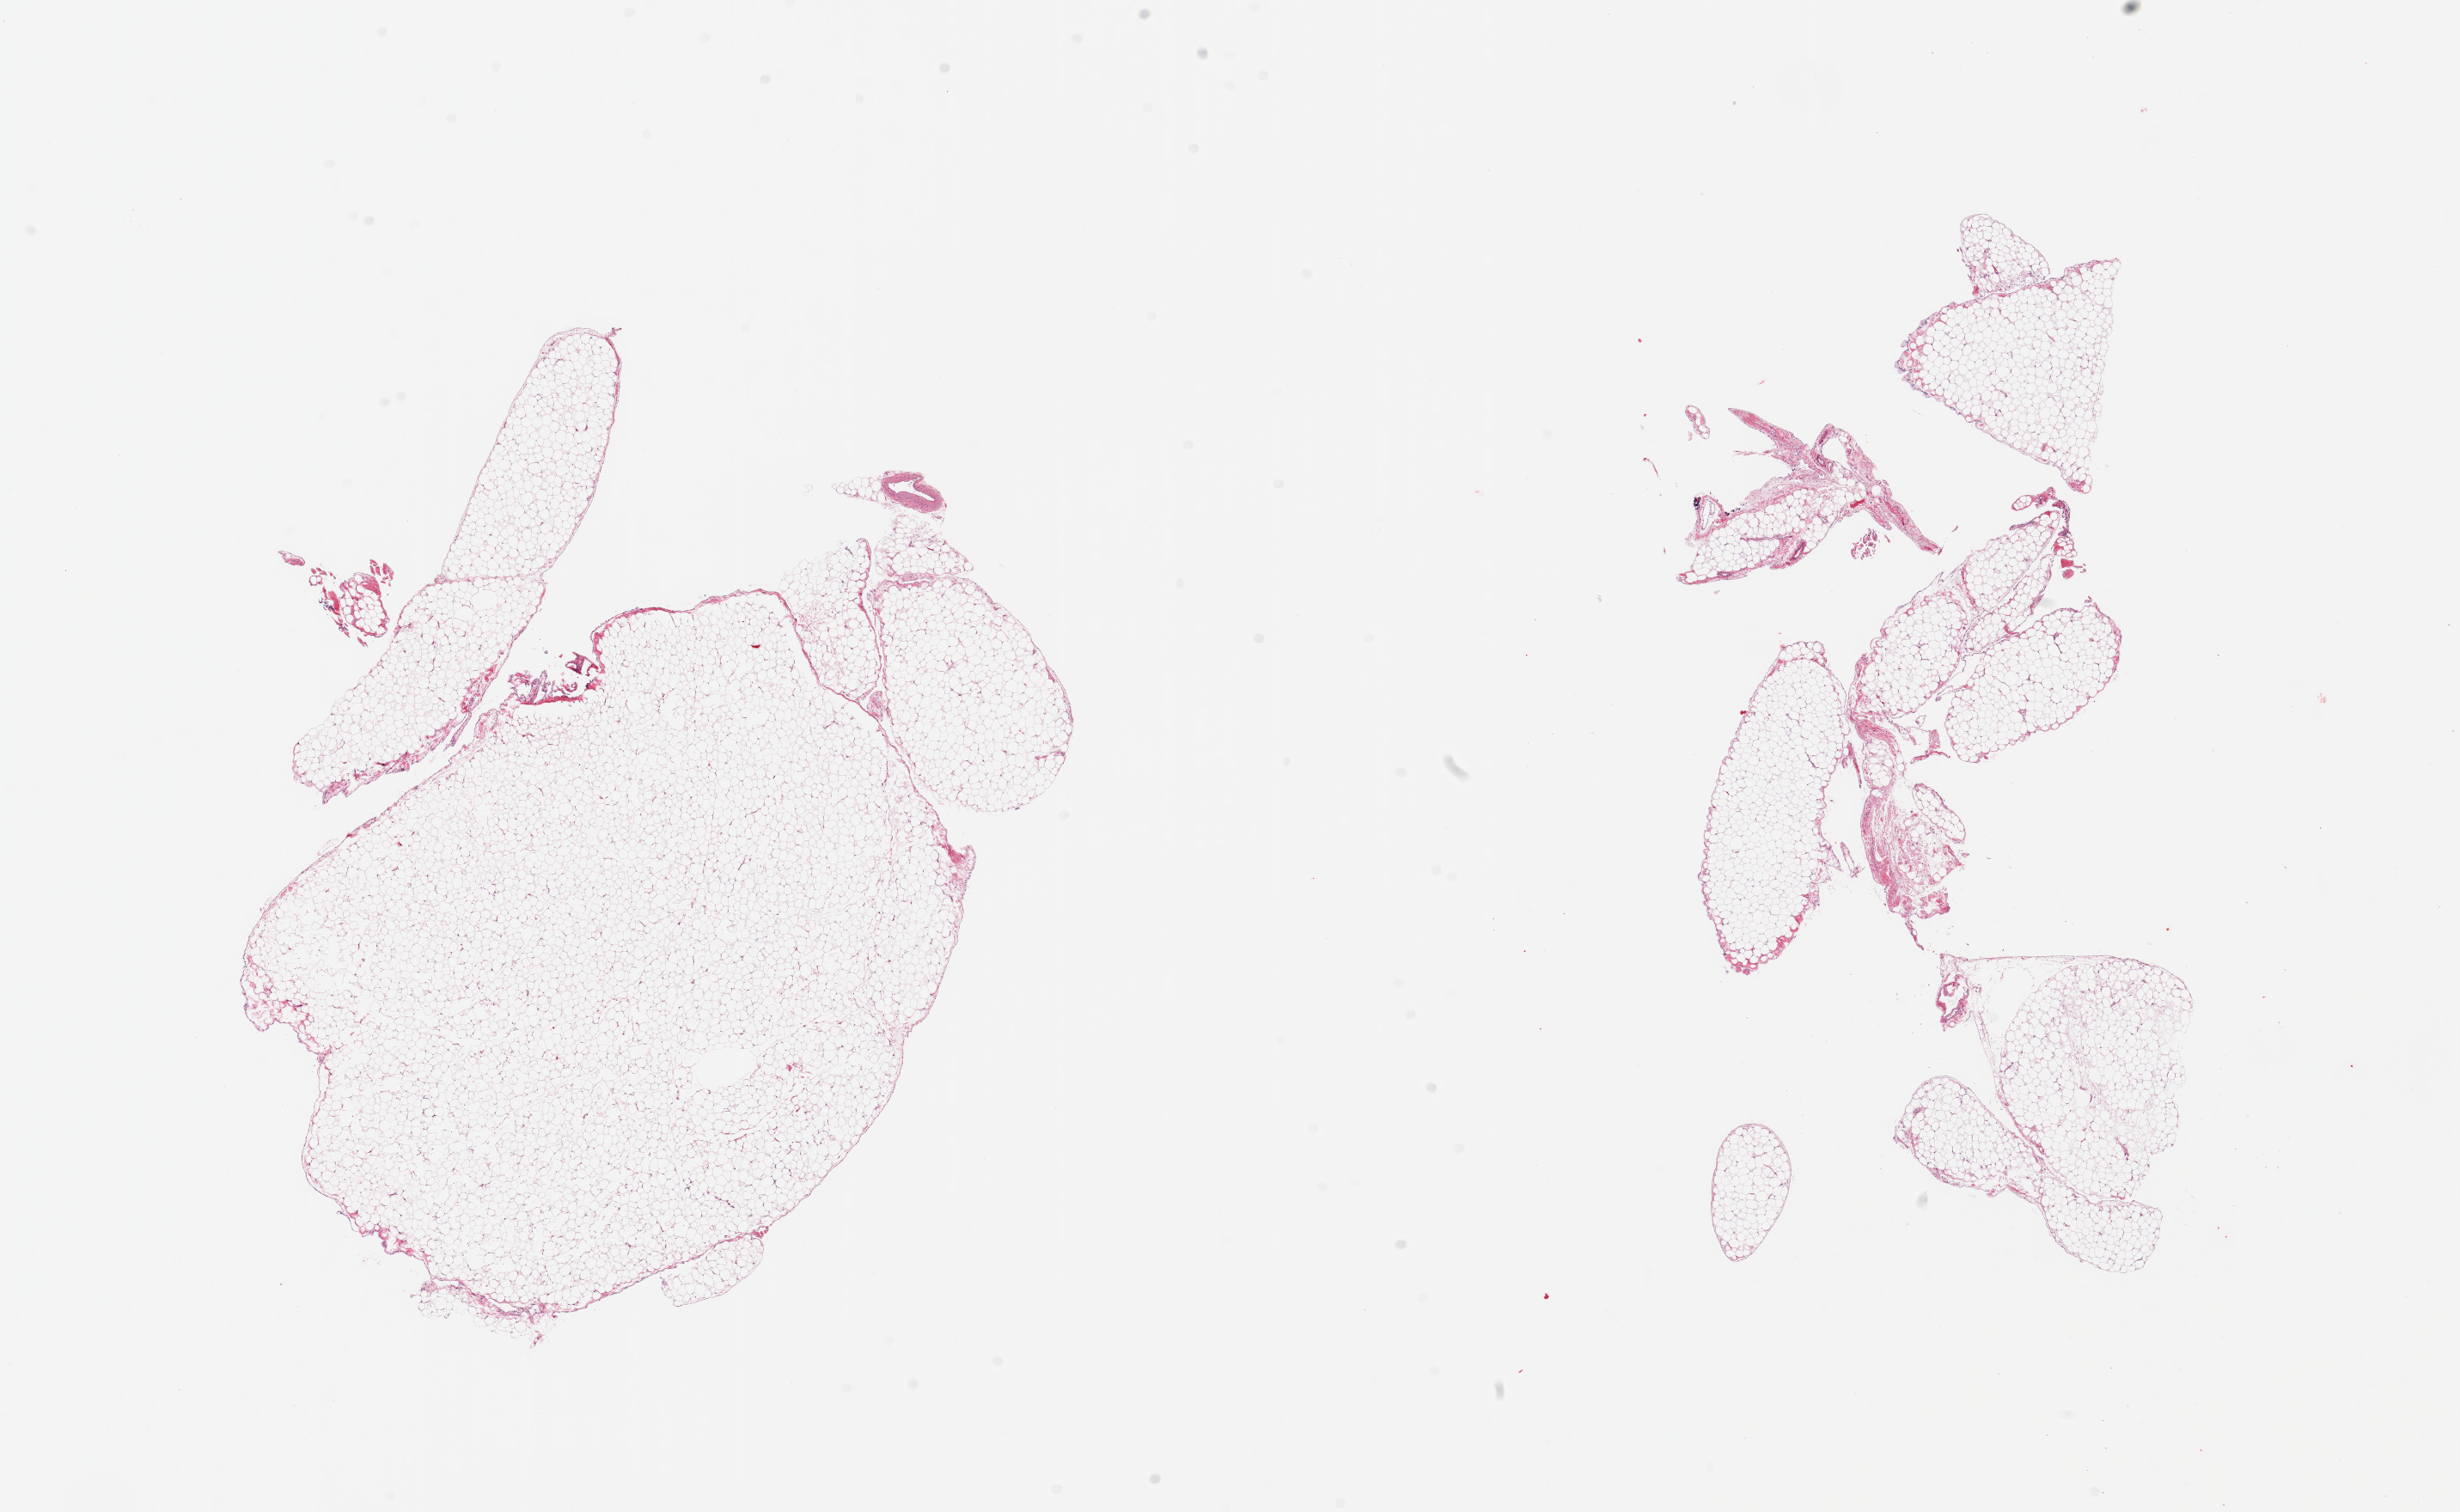
Digitized haematoxylin and eosin-stained section, brightfield, whole scanned area (about 22.6 x 13.9 mm) shown as a low-resolution overview. PAXgene-fixed paraffin-embedded (PFPE) section. Section of omentum (target tissue). Donor tissue sample.
Pathologist's review note for this sample: 2 pieces; 5% fibrovascular content.